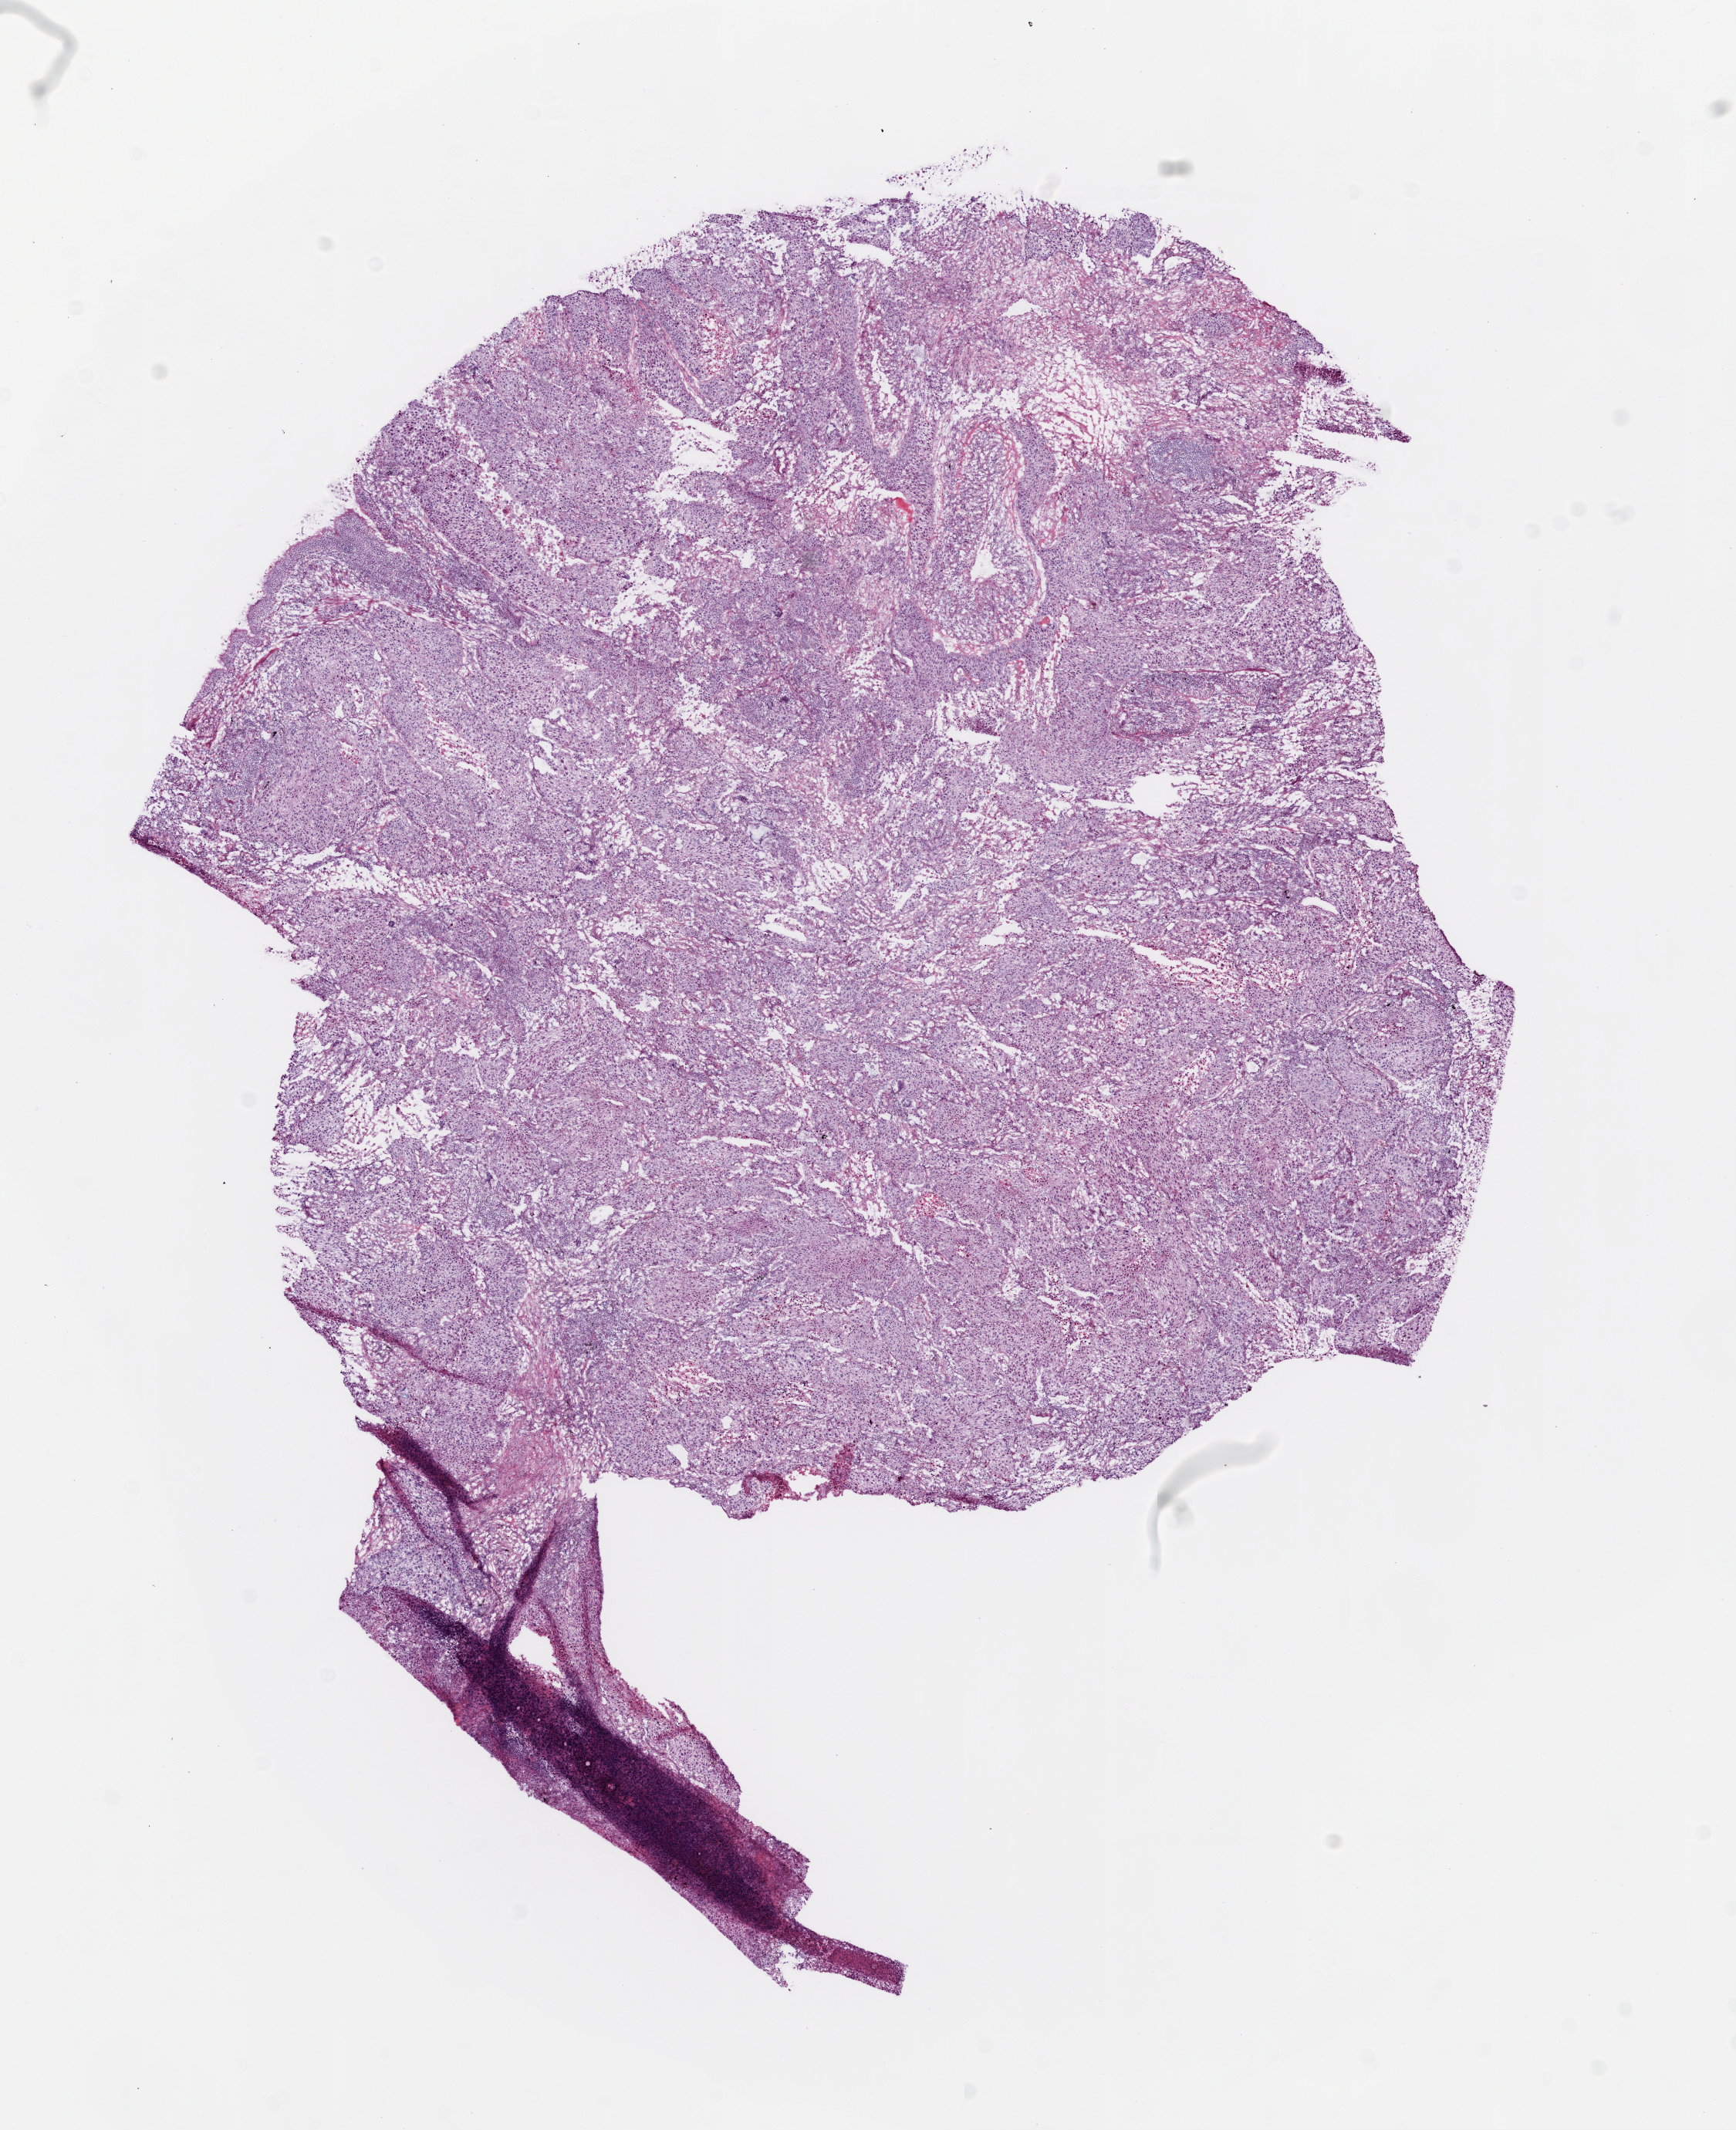
Digitized Hematoxylin and eosin (H&E) stained tissue section (whole slide), whole scanned area (about 9.0 x 11.1 mm) shown as a low-resolution overview. Frozen section from the top of the tissue portion. Sample: primary tumour, lung. Female, age 63 years at initial diagnosis. Slide review estimates, as recorded: tumour cells 83%, tumour nuclei 85%, normal cells 3%, stromal cells 10%, necrosis 5%.
* diagnosis: Squamous cell carcinoma, NOS
* AJCC pathologic stage: IB